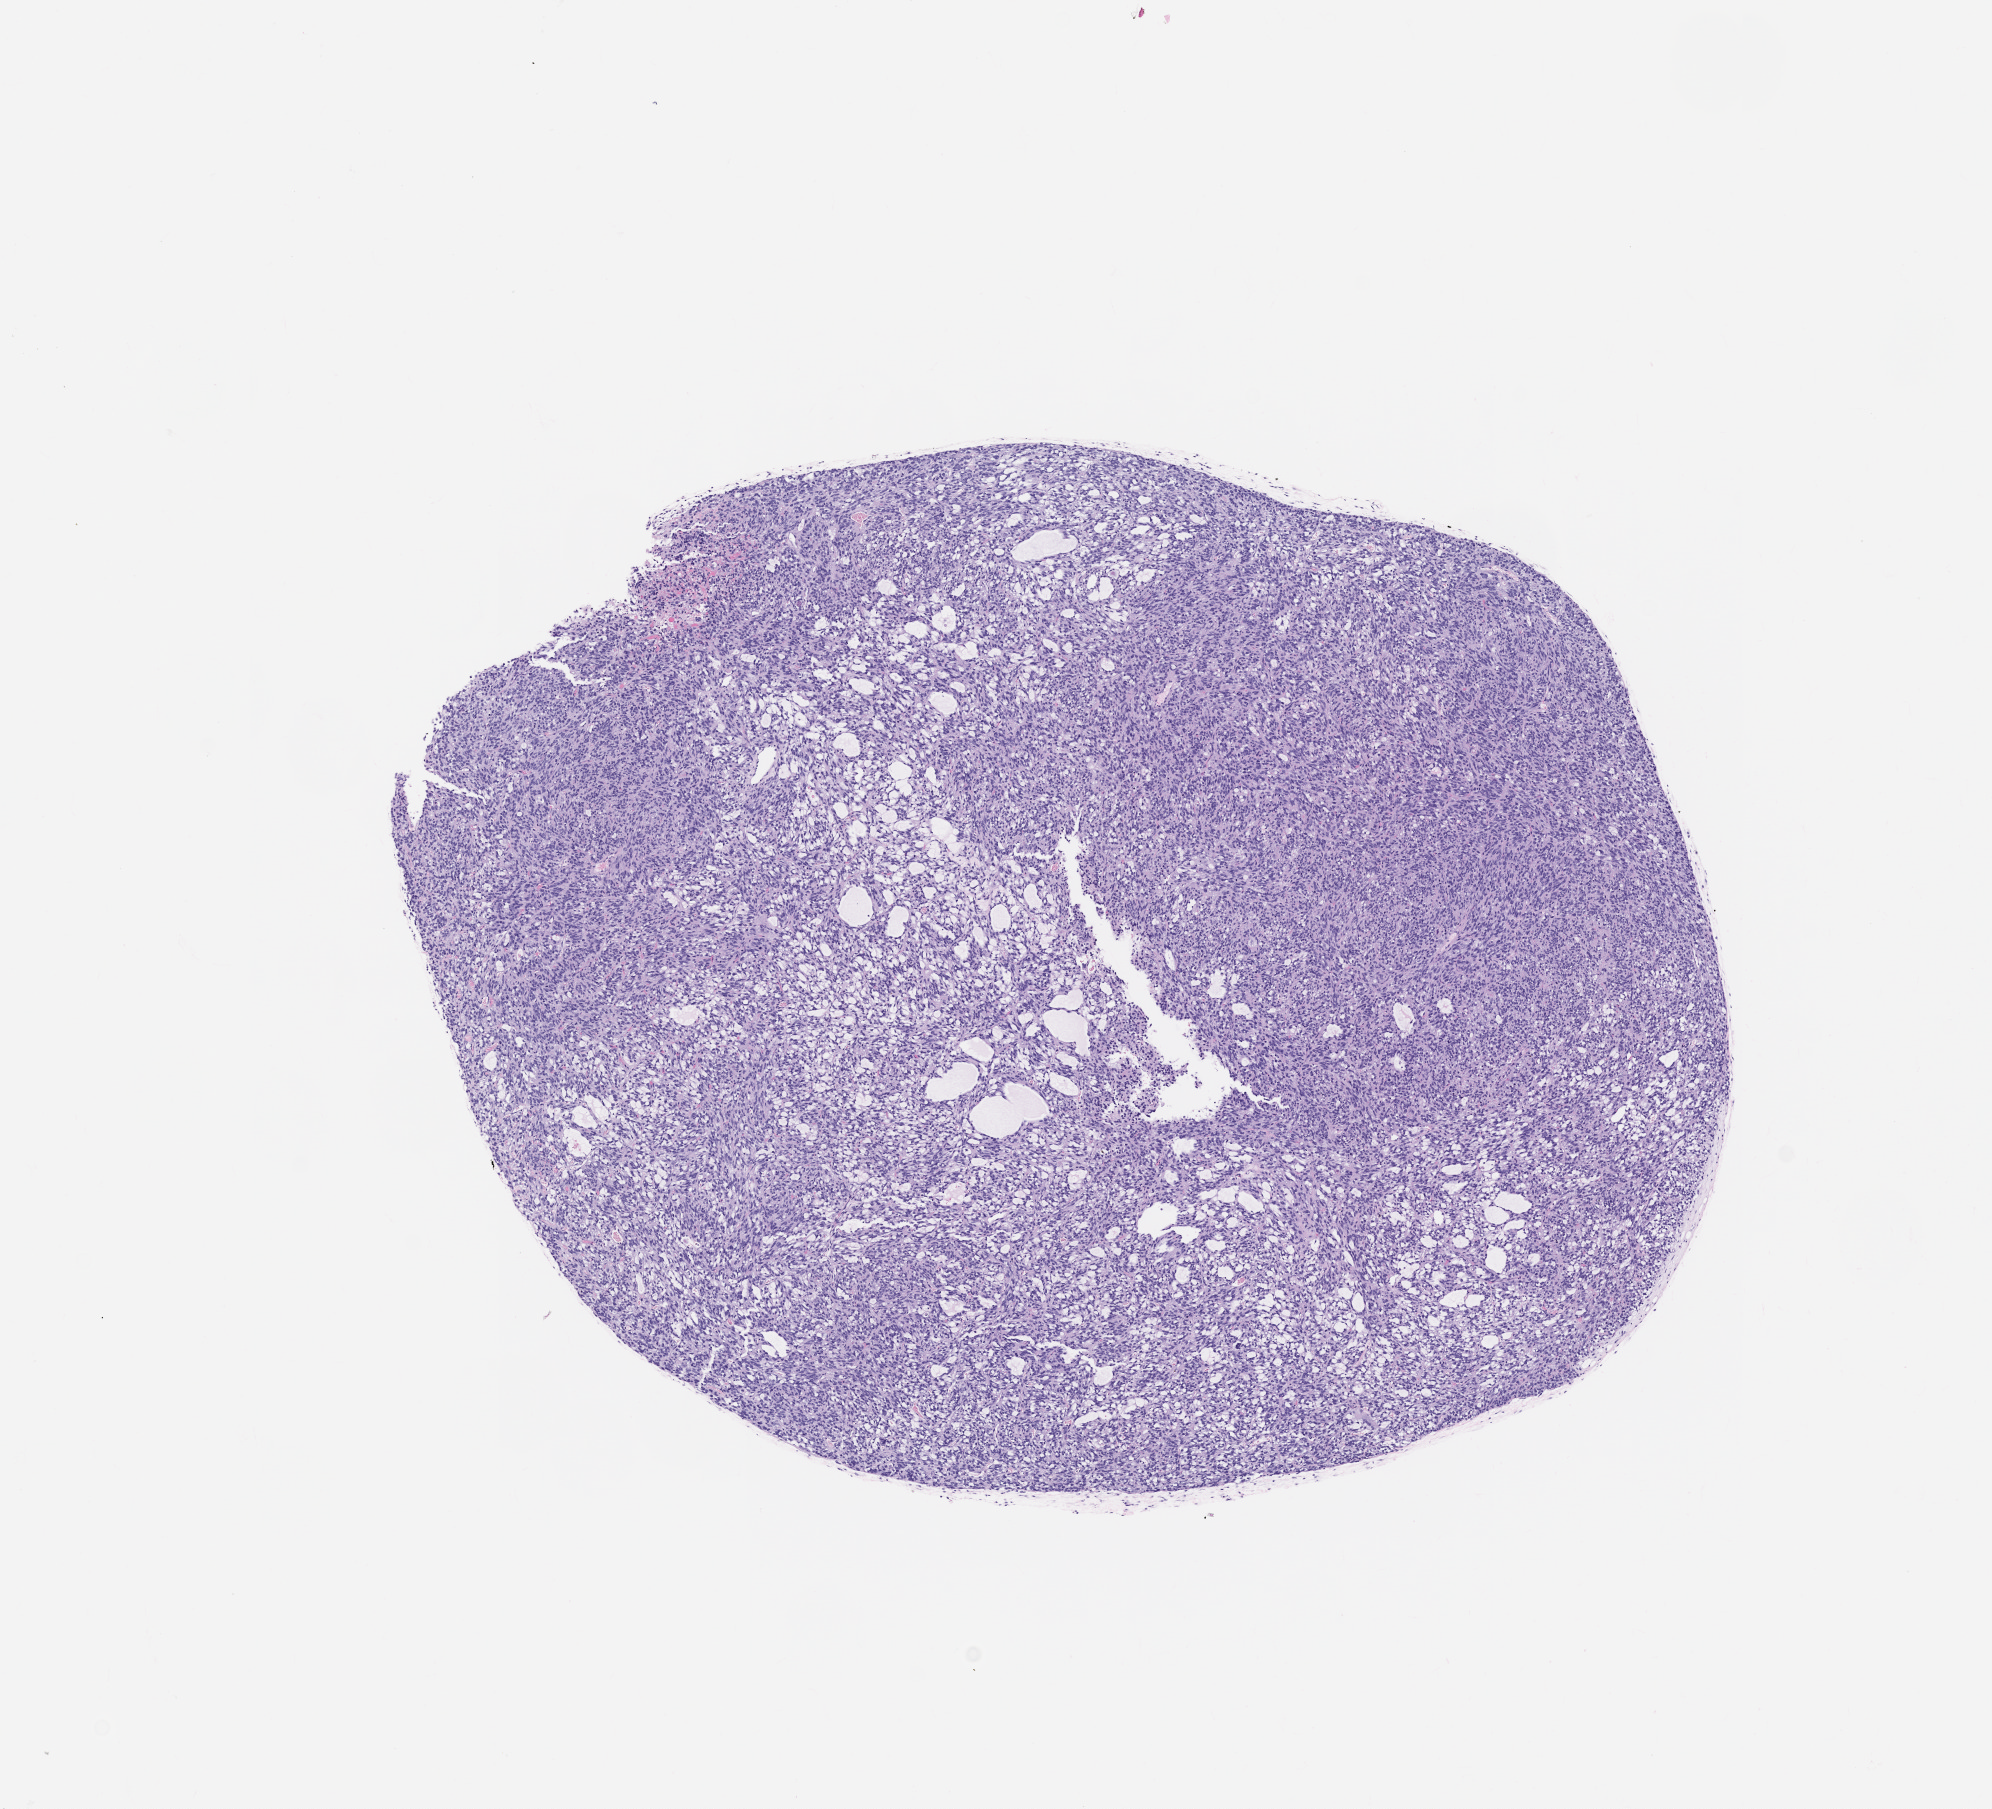
H&E whole-slide image of a patient-derived xenograft (PDX) tumor grown in a mouse, passage 1 — low-resolution overview of the scanned area, about 8.0 x 7.3 mm. Formalin-fixed paraffin-embedded section. Originating tumor site category: uterus.
Originating patient diagnosis: Leiomyosarcoma.